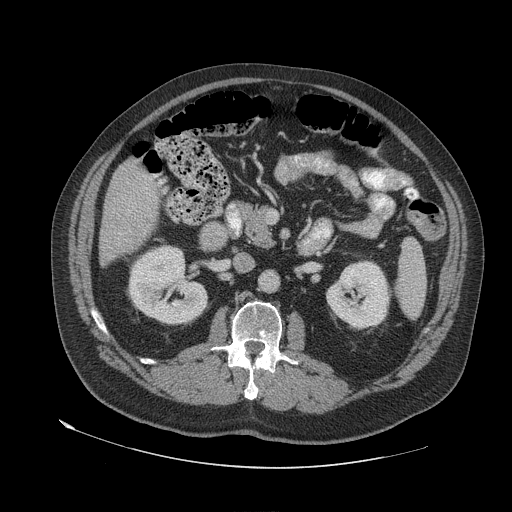
Contrast-enhanced abdominal CT (liver protocol), one axial slice. Position 19 of 79 along the scan axis. 140 kVp. Soft-tissue window (W 400 / L 40 HU). 2.5 mm slice thickness. 512 × 512 image matrix, field of view 480 × 480 mm. From the clinical record (not read from this slice): diagnosis: hepatocellular carcinoma (patient treated with transarterial chemoembolisation; whether this scan precedes or follows treatment is not stated here); TNM stage (as recorded): Stage-IVA; Child-Pugh class: A; tumour differentiation: well differentiated.
Structures marked on this image (semi-automatically segmented with operator editing):
- liver parenchyma outside the tumour (the mass and vessels are separate outlines, so this box may not span the whole liver): bounding box (x1, y1, x2, y2) in pixels: (98, 161, 164, 265)
- liver vessels: (154, 175, 162, 184)